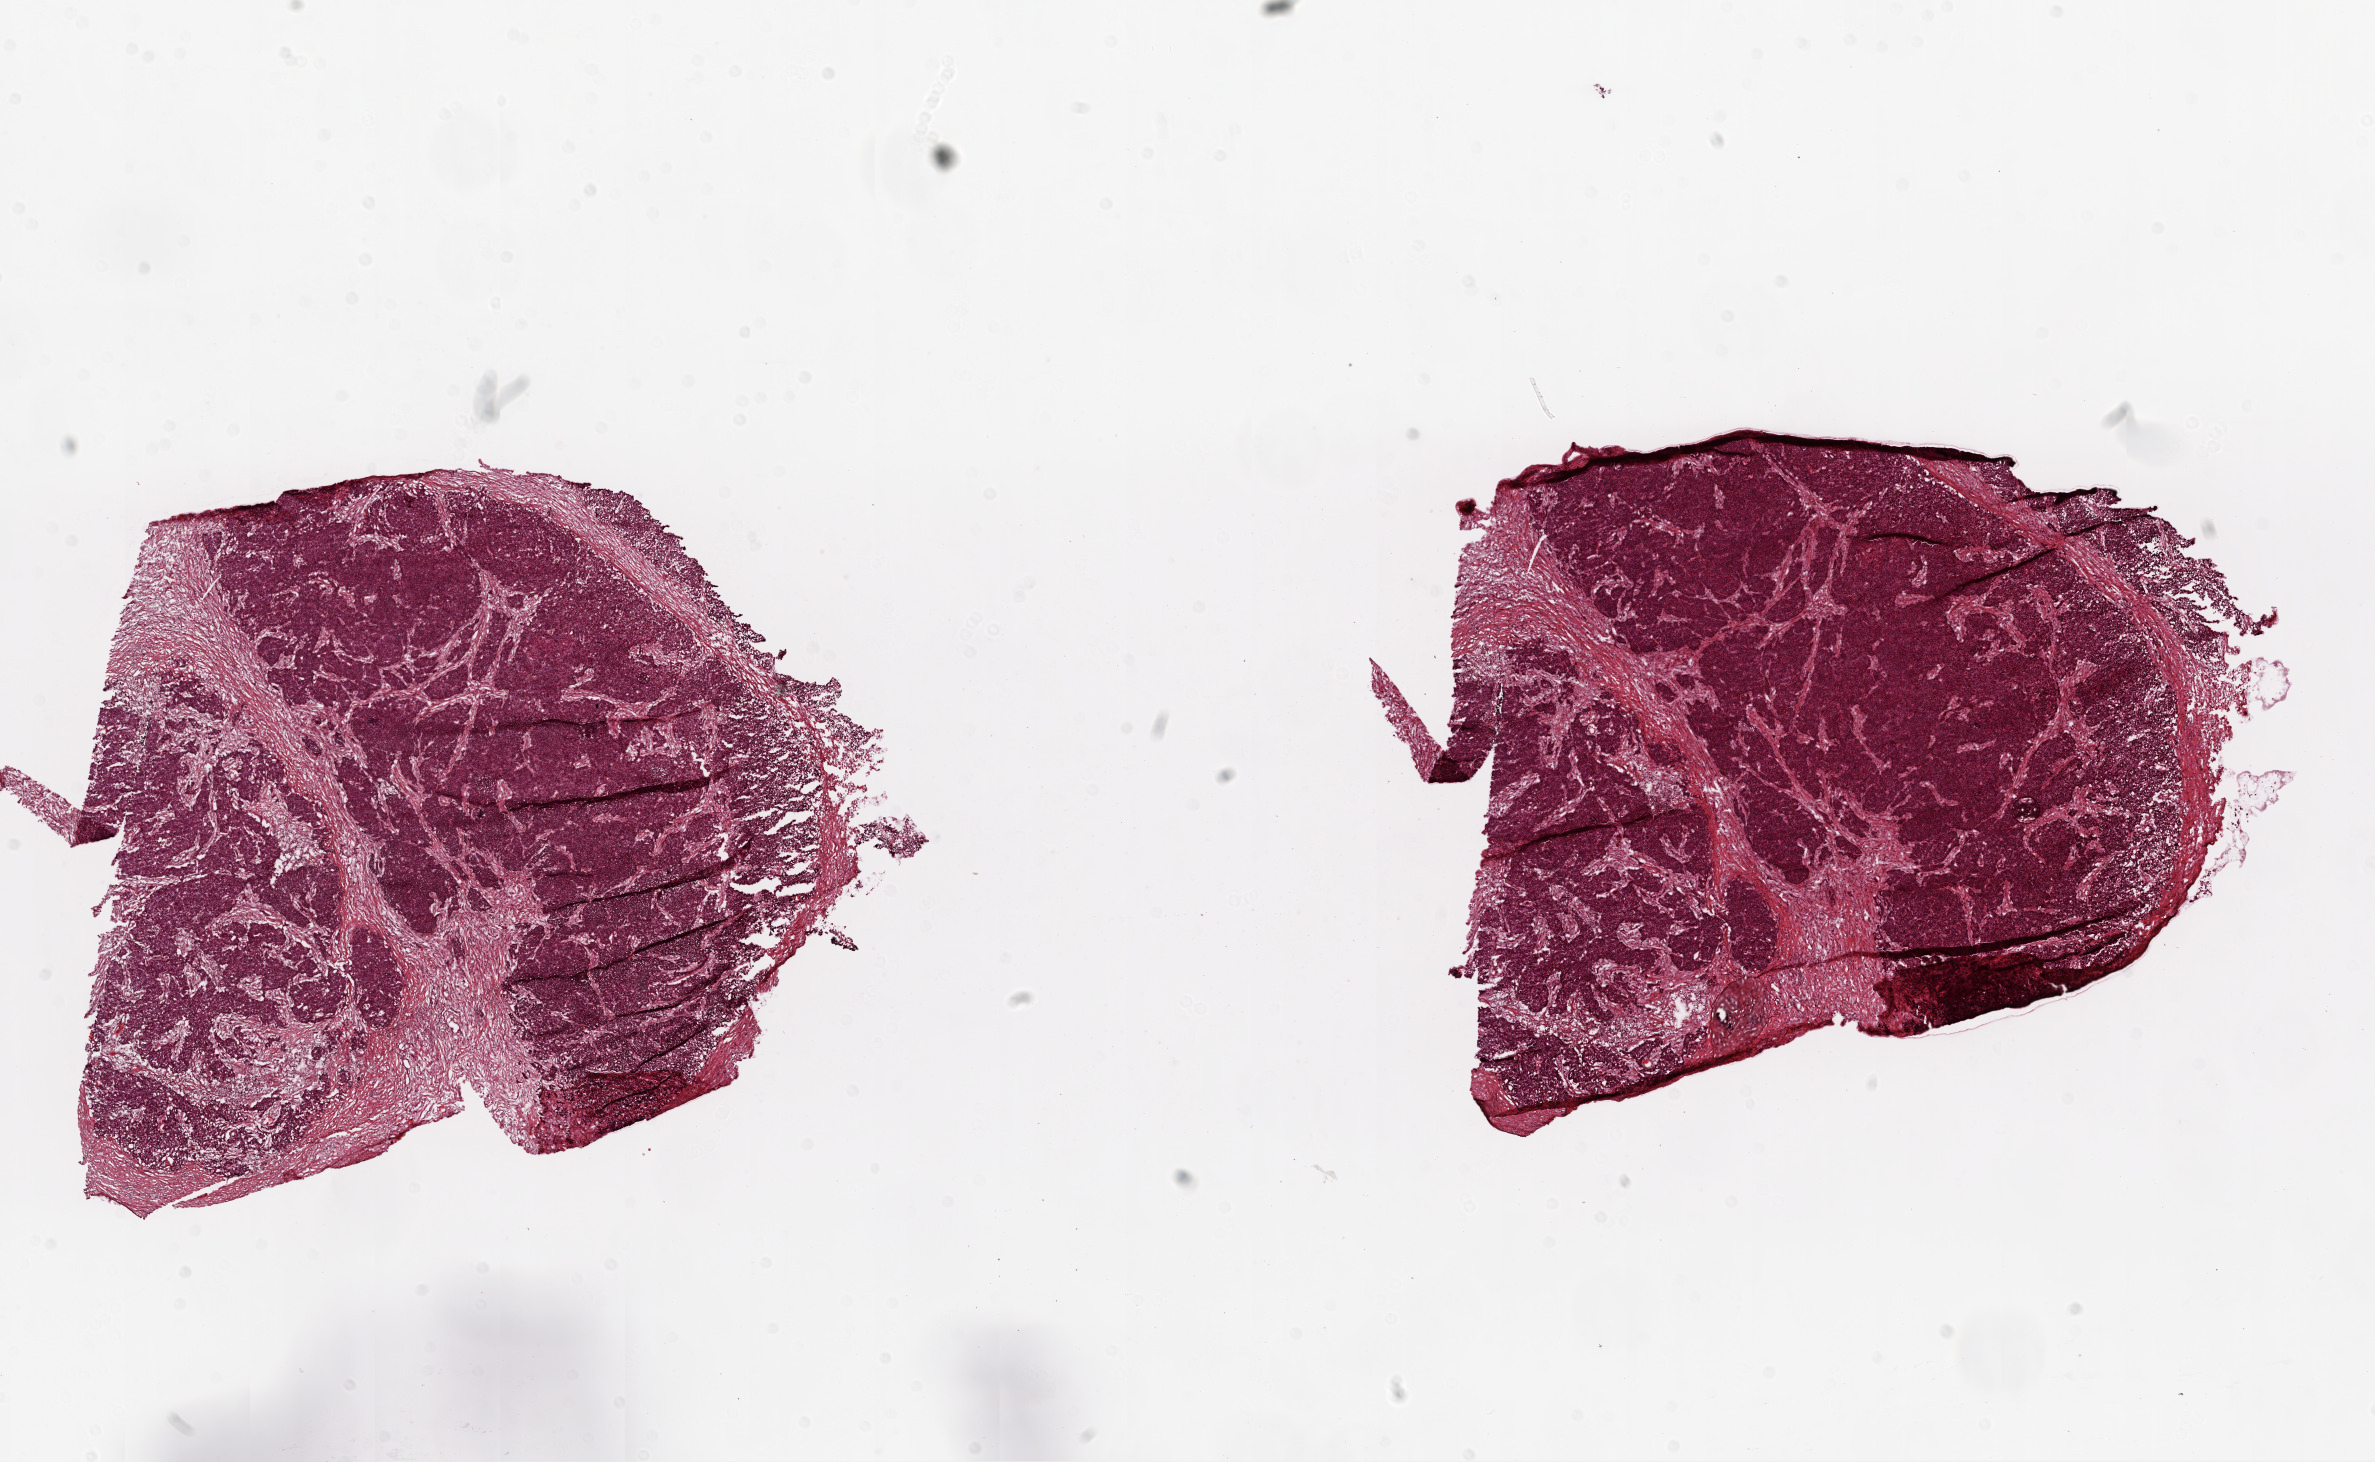
Whole-slide histology image, H&E-stained, shown as a low-resolution overview of the whole scanned area (about 19.1 x 11.7 mm, acquisition: 20x scan); frozen section from the top of the tissue portion; sample: primary tumour, ovary. Patient: female, age at initial diagnosis 45 years. Histologic grade: G3 (poorly differentiated). Composition of this section per pathologist review: tumour cells 70%, tumour nuclei 70%, normal cells 0%, stromal cells 10%, necrosis 20%. Inflammatory infiltration, as recorded: lymphocyte infiltration 0%, monocyte infiltration 0%, neutrophil infiltration 20%.
FIGO stage: IIIC. Diagnosis: Serous cystadenocarcinoma, NOS.